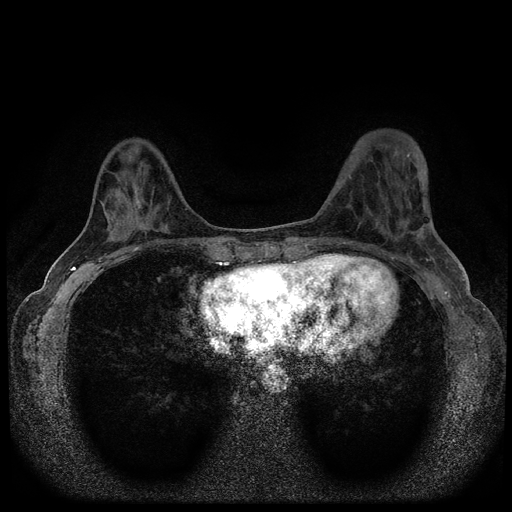
Breast MRI (dynamic contrast-enhanced, multi-phase), one axial slice; position 37 of 116 along the scan axis; dynamic contrast-enhanced series, time point 2 of 5 at this slice position (early post-contrast); 1.5 T; TE 2.7 ms, TR 5.6 ms; 512 × 512 image matrix, field of view 310 × 310 mm. Patient: female, 40 years.
Outlined on this slice (semi-automatic segmentation, software-assisted and operator-edited):
- breast lesion (labelled benign in the annotation): box from (x=130, y=183) to (x=145, y=210) px